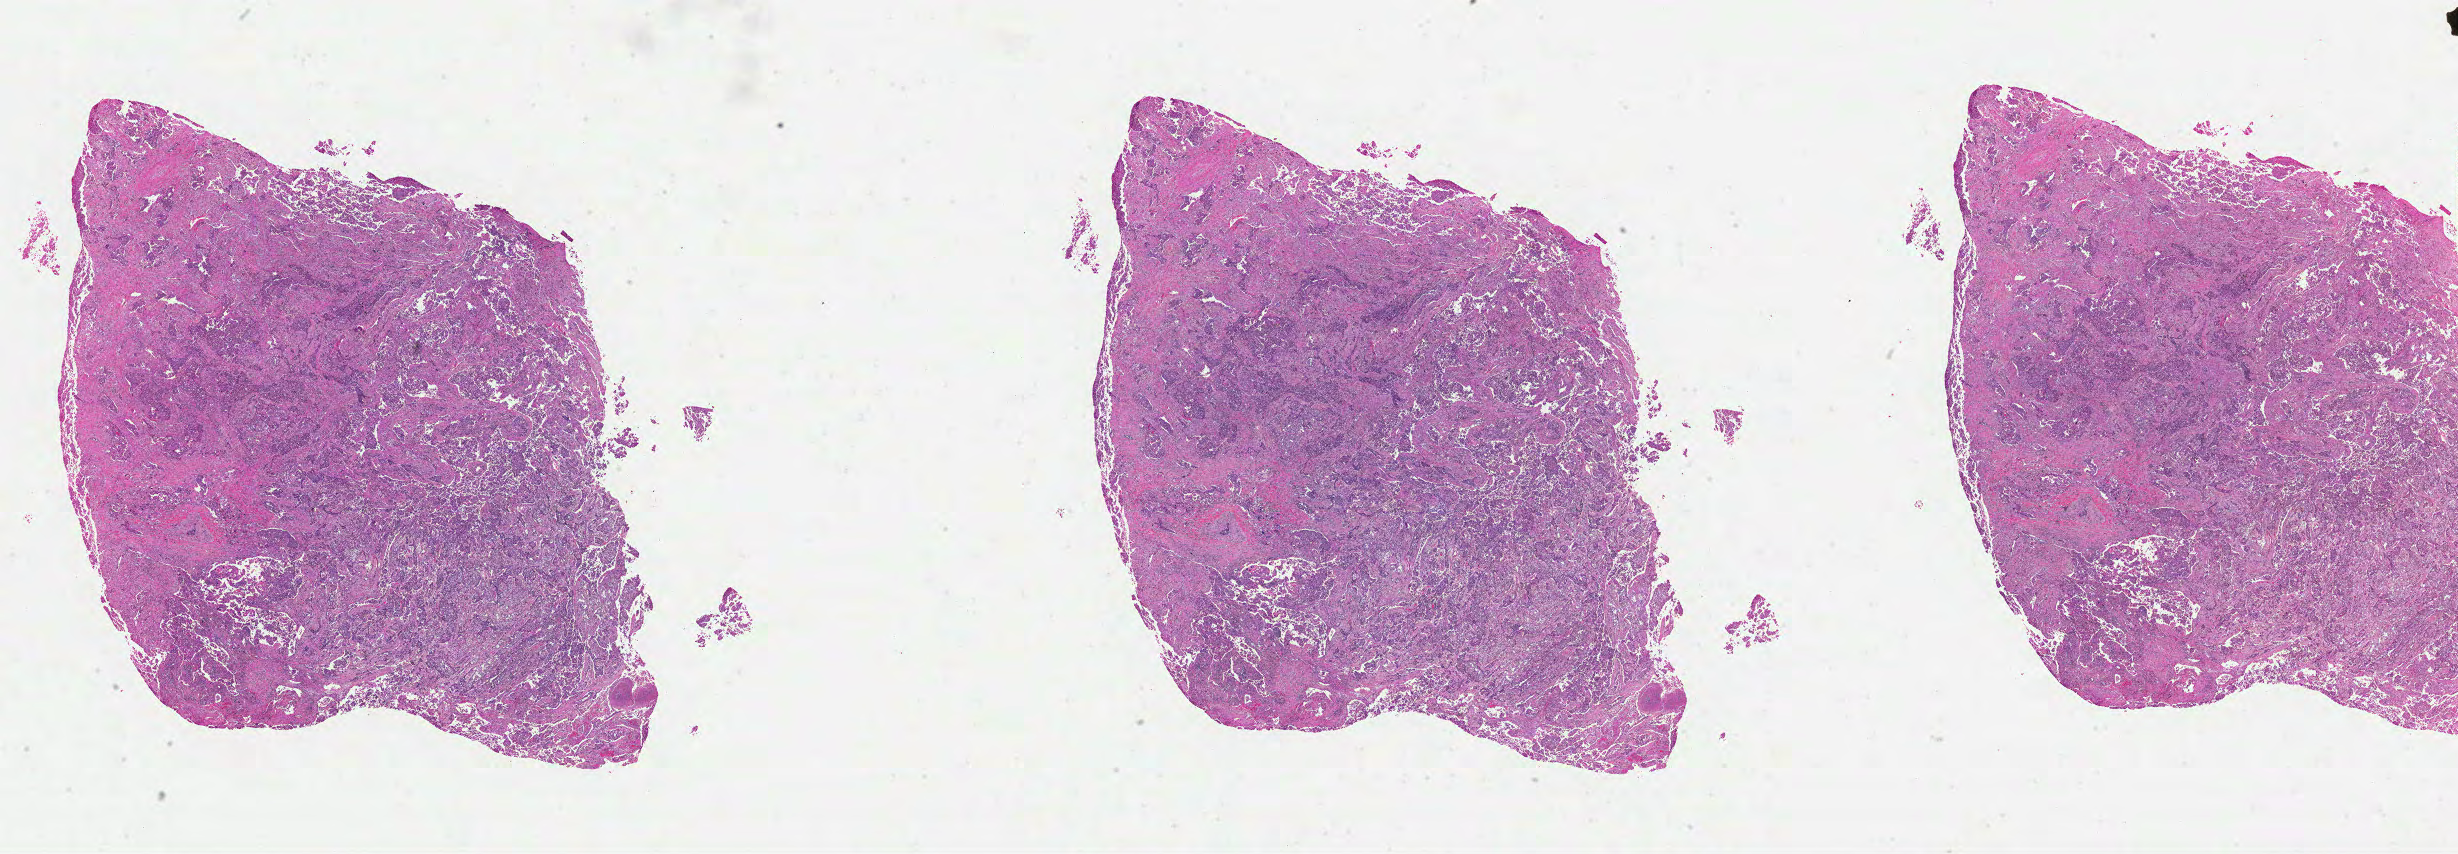
Digitized H&E tissue section (whole slide) — shown as a low-resolution overview of the whole scanned area (about 39.6 x 13.8 mm, slide scanned at 40x). FFPE section. Primary tumour sample from the lung. Patient: female, age at initial diagnosis 57 years.
Histologic diagnosis: Adenocarcinoma, NOS.